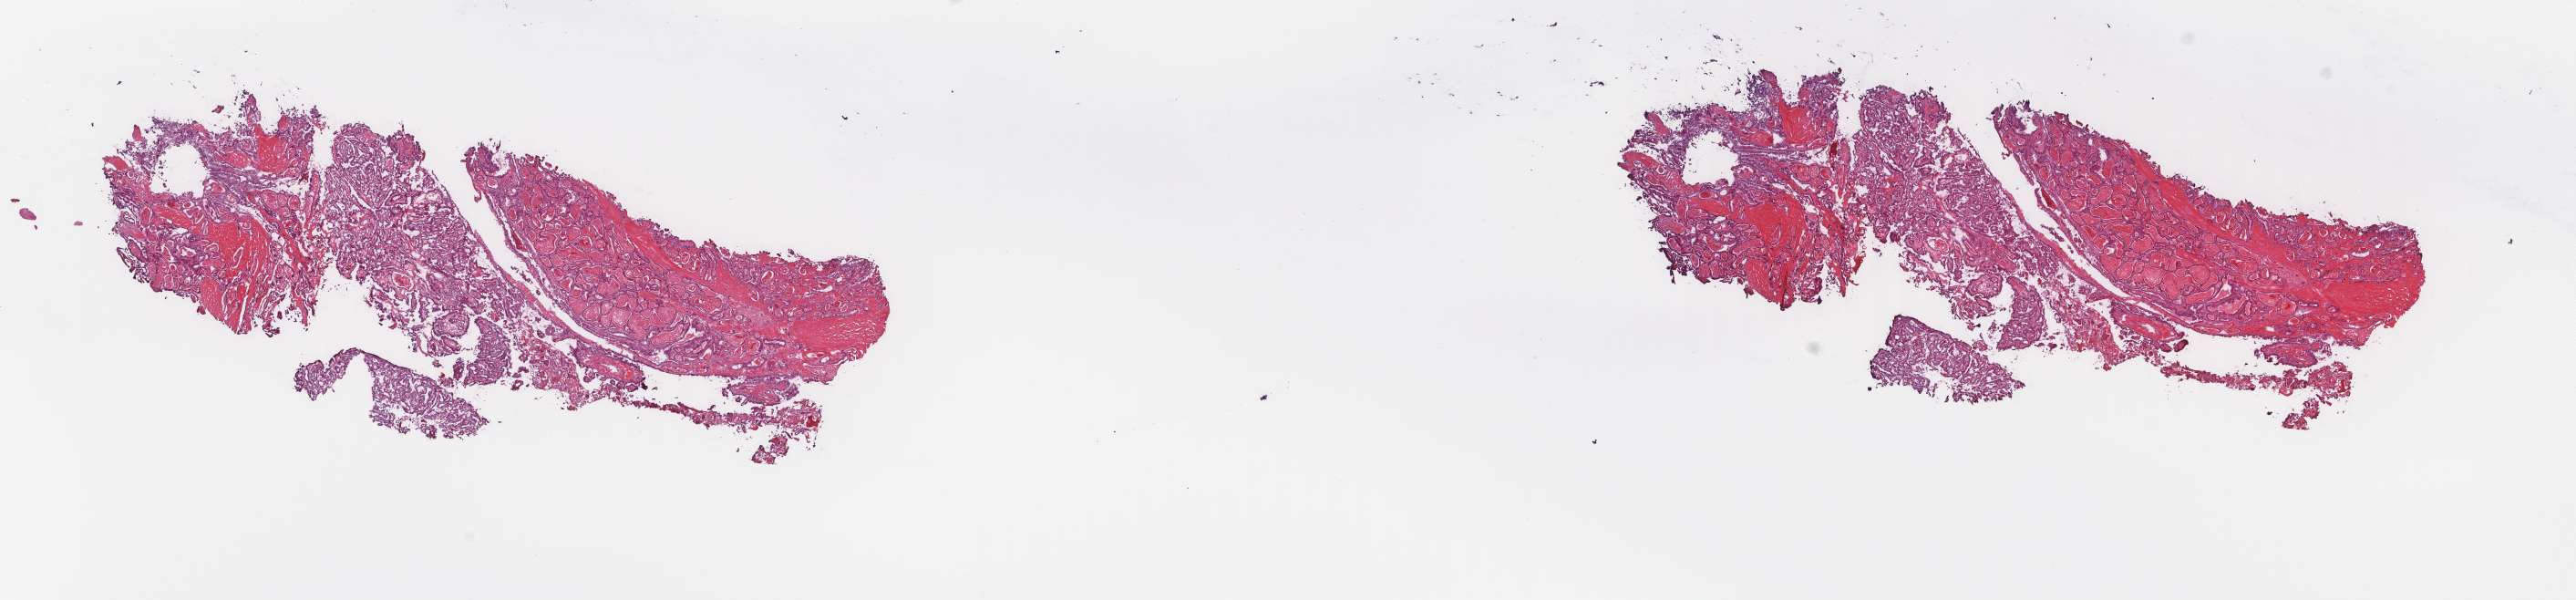
H&E-stained whole-slide image — a low-resolution overview of the entire scanned area, about 22.4 x 5.2 mm (slide scanned at 40x). Frozen section from the top of the tissue portion. Sample: primary tumour, thyroid. Male, age 52 years at initial diagnosis. Slide review estimates, as recorded: tumour cells 65%, tumour nuclei 100%, normal cells 0%, stromal cells 35%, necrosis 0%. Inflammatory infiltration, as recorded: lymphocyte infiltration 1%, monocyte infiltration 0%, neutrophil infiltration 0%.
Histologic diagnosis: Papillary carcinoma, columnar cell. TNM: T3 N1a M0. AJCC pathologic stage: III. Lymph nodes positive (case pathology): 1 of 1 examined.